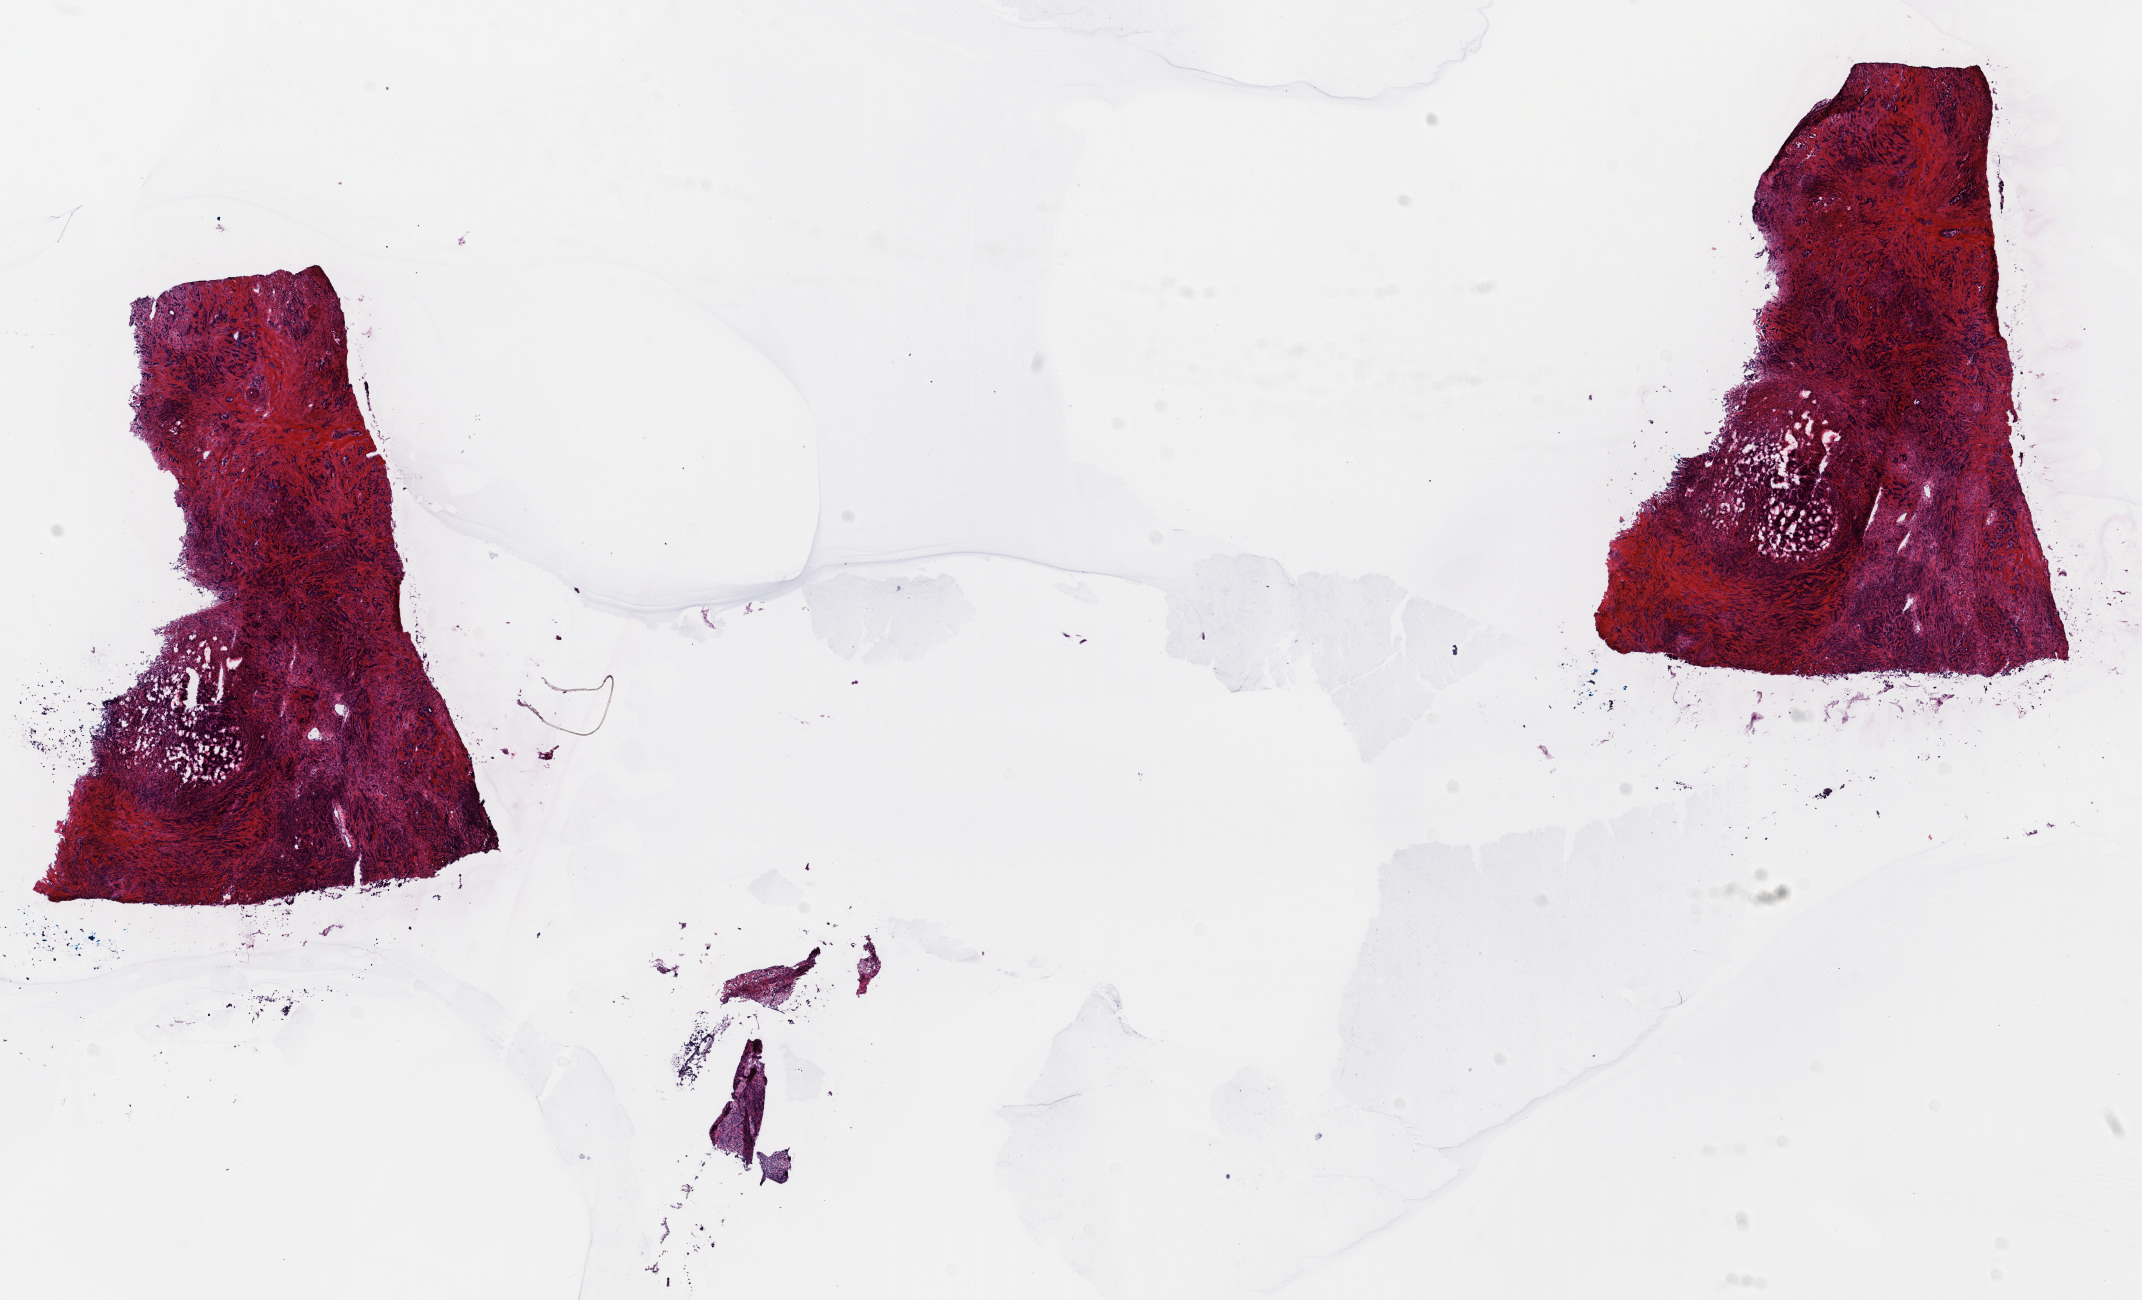
Digitized Hematoxylin and eosin (H&E) stained tissue section (whole slide), a low-resolution overview of the entire scanned area, about 16.8 x 10.2 mm (slide scanned at 40x). Frozen section. Breast, primary tumour sample. Female patient; age at initial diagnosis 71 years. Composition of this section per pathologist review: tumour cells 100%, tumour nuclei 70%, normal cells 0%, stromal cells 0%, necrosis 0%. Infiltration values recorded for this section: lymphocyte infiltration 0%, monocyte infiltration 0%, neutrophil infiltration 0%.
Diagnosis: Infiltrating duct carcinoma, NOS. TNM: T2 N0 MX. AJCC pathologic stage: IIA (7th edition). Lymph nodes positive (case pathology): 0 of 7 examined.